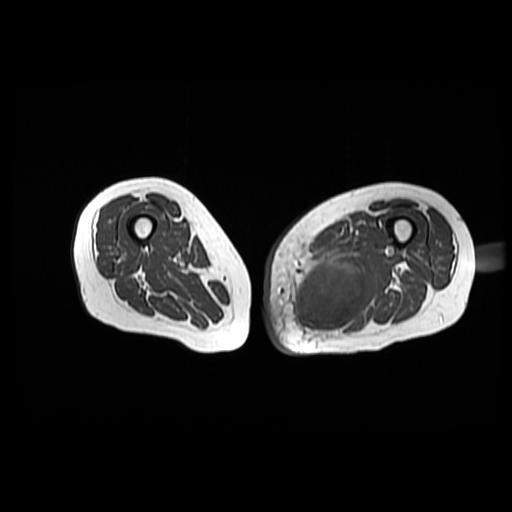
MRI of an extremity soft-tissue mass, one axial slice. Position 35 of 42 along the scan axis. 6 mm slice thickness. 512 × 512 image matrix, field of view 420 × 420 mm. Female patient. From the clinical record (not read from this slice): histological type: pleomorphic leiomyosarcoma; grade: high; site of the primary tumour: left thigh.
Structures marked on this image (outlined manually by an expert reader):
- gross tumour volume including surrounding oedema: box from (x=294, y=240) to (x=376, y=337) px
- gross tumour volume (mass): (x=294, y=260)–(x=366, y=337)